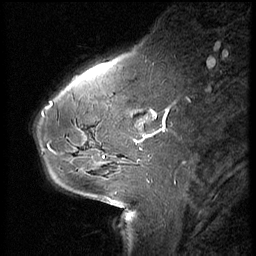
Breast MRI (dynamic contrast-enhanced), one sagittal slice. Slice 19 of 66 in the series (ordered by position). 3 images stored at this slice position (order not interpretable as contrast timing). 1.5 T. TE 4.2 ms, TR 8.9 ms. 2.5 mm slice thickness. 256 × 256 image matrix, field of view 200 × 200 mm. Patient: female, 54 years. From the clinical record (not read from this slice): setting: breast cancer imaged before/during neoadjuvant chemotherapy; receptor status: HR-positive, HER2-negative.
Structures marked on this image (semi-automatic segmentation, software-assisted and operator-edited):
- analysis volume of interest (the breast-tissue region the enhancement analysis was run in; not a lesion): box from (x=61, y=104) to (x=146, y=171) px
- tumour enhancement mask (voxels above the 140 % enhancement threshold inside the analysis volume of interest): (x=135, y=136)–(x=144, y=151)